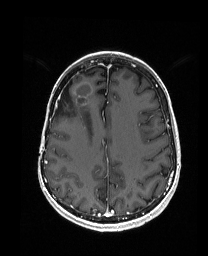
Brain MRI from a brain-tumour surgery series, one axial slice; slice 65 of 192 in the series (ordered by position); T1-weighted post-contrast; 1 mm slice thickness; 208 × 256 image matrix. Case-level facts recorded for this patient, not image findings: histopathology: Metastatic Carcinoma from Breast primary.
Annotated regions visible in this slice (outlined manually by an expert reader):
- previous resection cavity: box from (x=54, y=82) to (x=71, y=115) px
- tumour: (x=82, y=81)–(x=100, y=114)